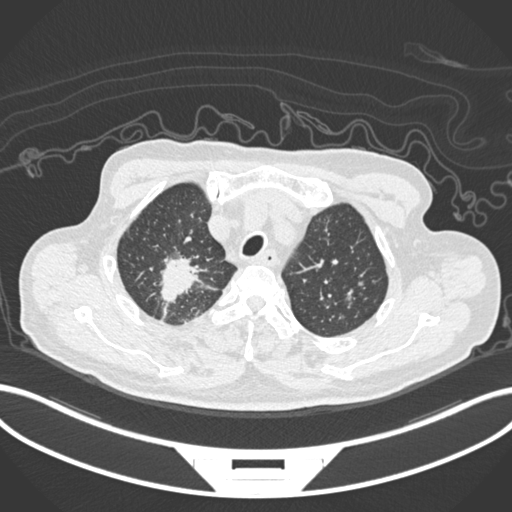
Chest CT, one axial slice. Slice 178 of 207 in the series (ordered by position). Reconstruction kernel B30f. Lung window (W 1500 / L -600 HU). 1 mm slice thickness. 512 × 512 image matrix. Patient: male, 69 years. From the clinical record (not read from this slice): clinical TNM (as recorded): T1c N1 M1.
Annotated regions visible in this slice (bounding box drawn by a radiologist):
- lung tumour (recorded histology: adenocarcinoma): bounding box [x1, y1, x2, y2] px = [158, 252, 212, 311]